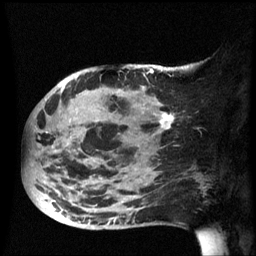
Breast MRI (dynamic contrast-enhanced), one sagittal slice. Position 24 of 60 along the scan axis. Dynamic contrast-enhanced series, image 2 of 3 at this slice position (ordered by acquisition). 1.5 T. TE 4.2 ms, TR 8.4 ms. 2.5 mm slice thickness. 256 × 256 image matrix, field of view 220 × 220 mm. Female patient, age 49 years.
Structures marked on this image (semi-automatically segmented with operator editing):
- analysis volume of interest (the breast-tissue region the enhancement analysis was run in; not a lesion): bounding box <25,72,175,231> (left, top, right, bottom; pixels)
- tumour enhancement mask (voxels above the 70 % enhancement threshold inside the analysis volume of interest): <55,72,175,225>